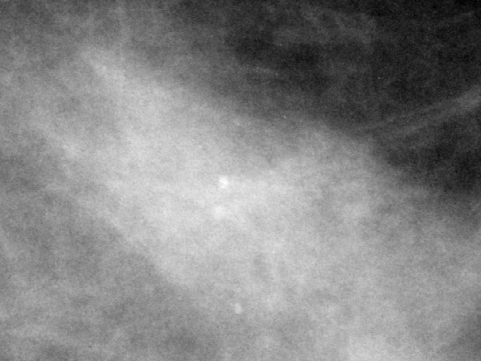
Region of interest cut from a scanned film mammogram (one marked finding), left breast, CC view, BI-RADS breast density category 3 (scale 1–4).
Marked abnormality: calcifications, morphology punctate, distribution clustered; BI-RADS assessment category 2; subtlety rating 3 on a 1 (subtle) to 5 (obvious) scale; benign; no additional work-up was recommended (benign without callback).